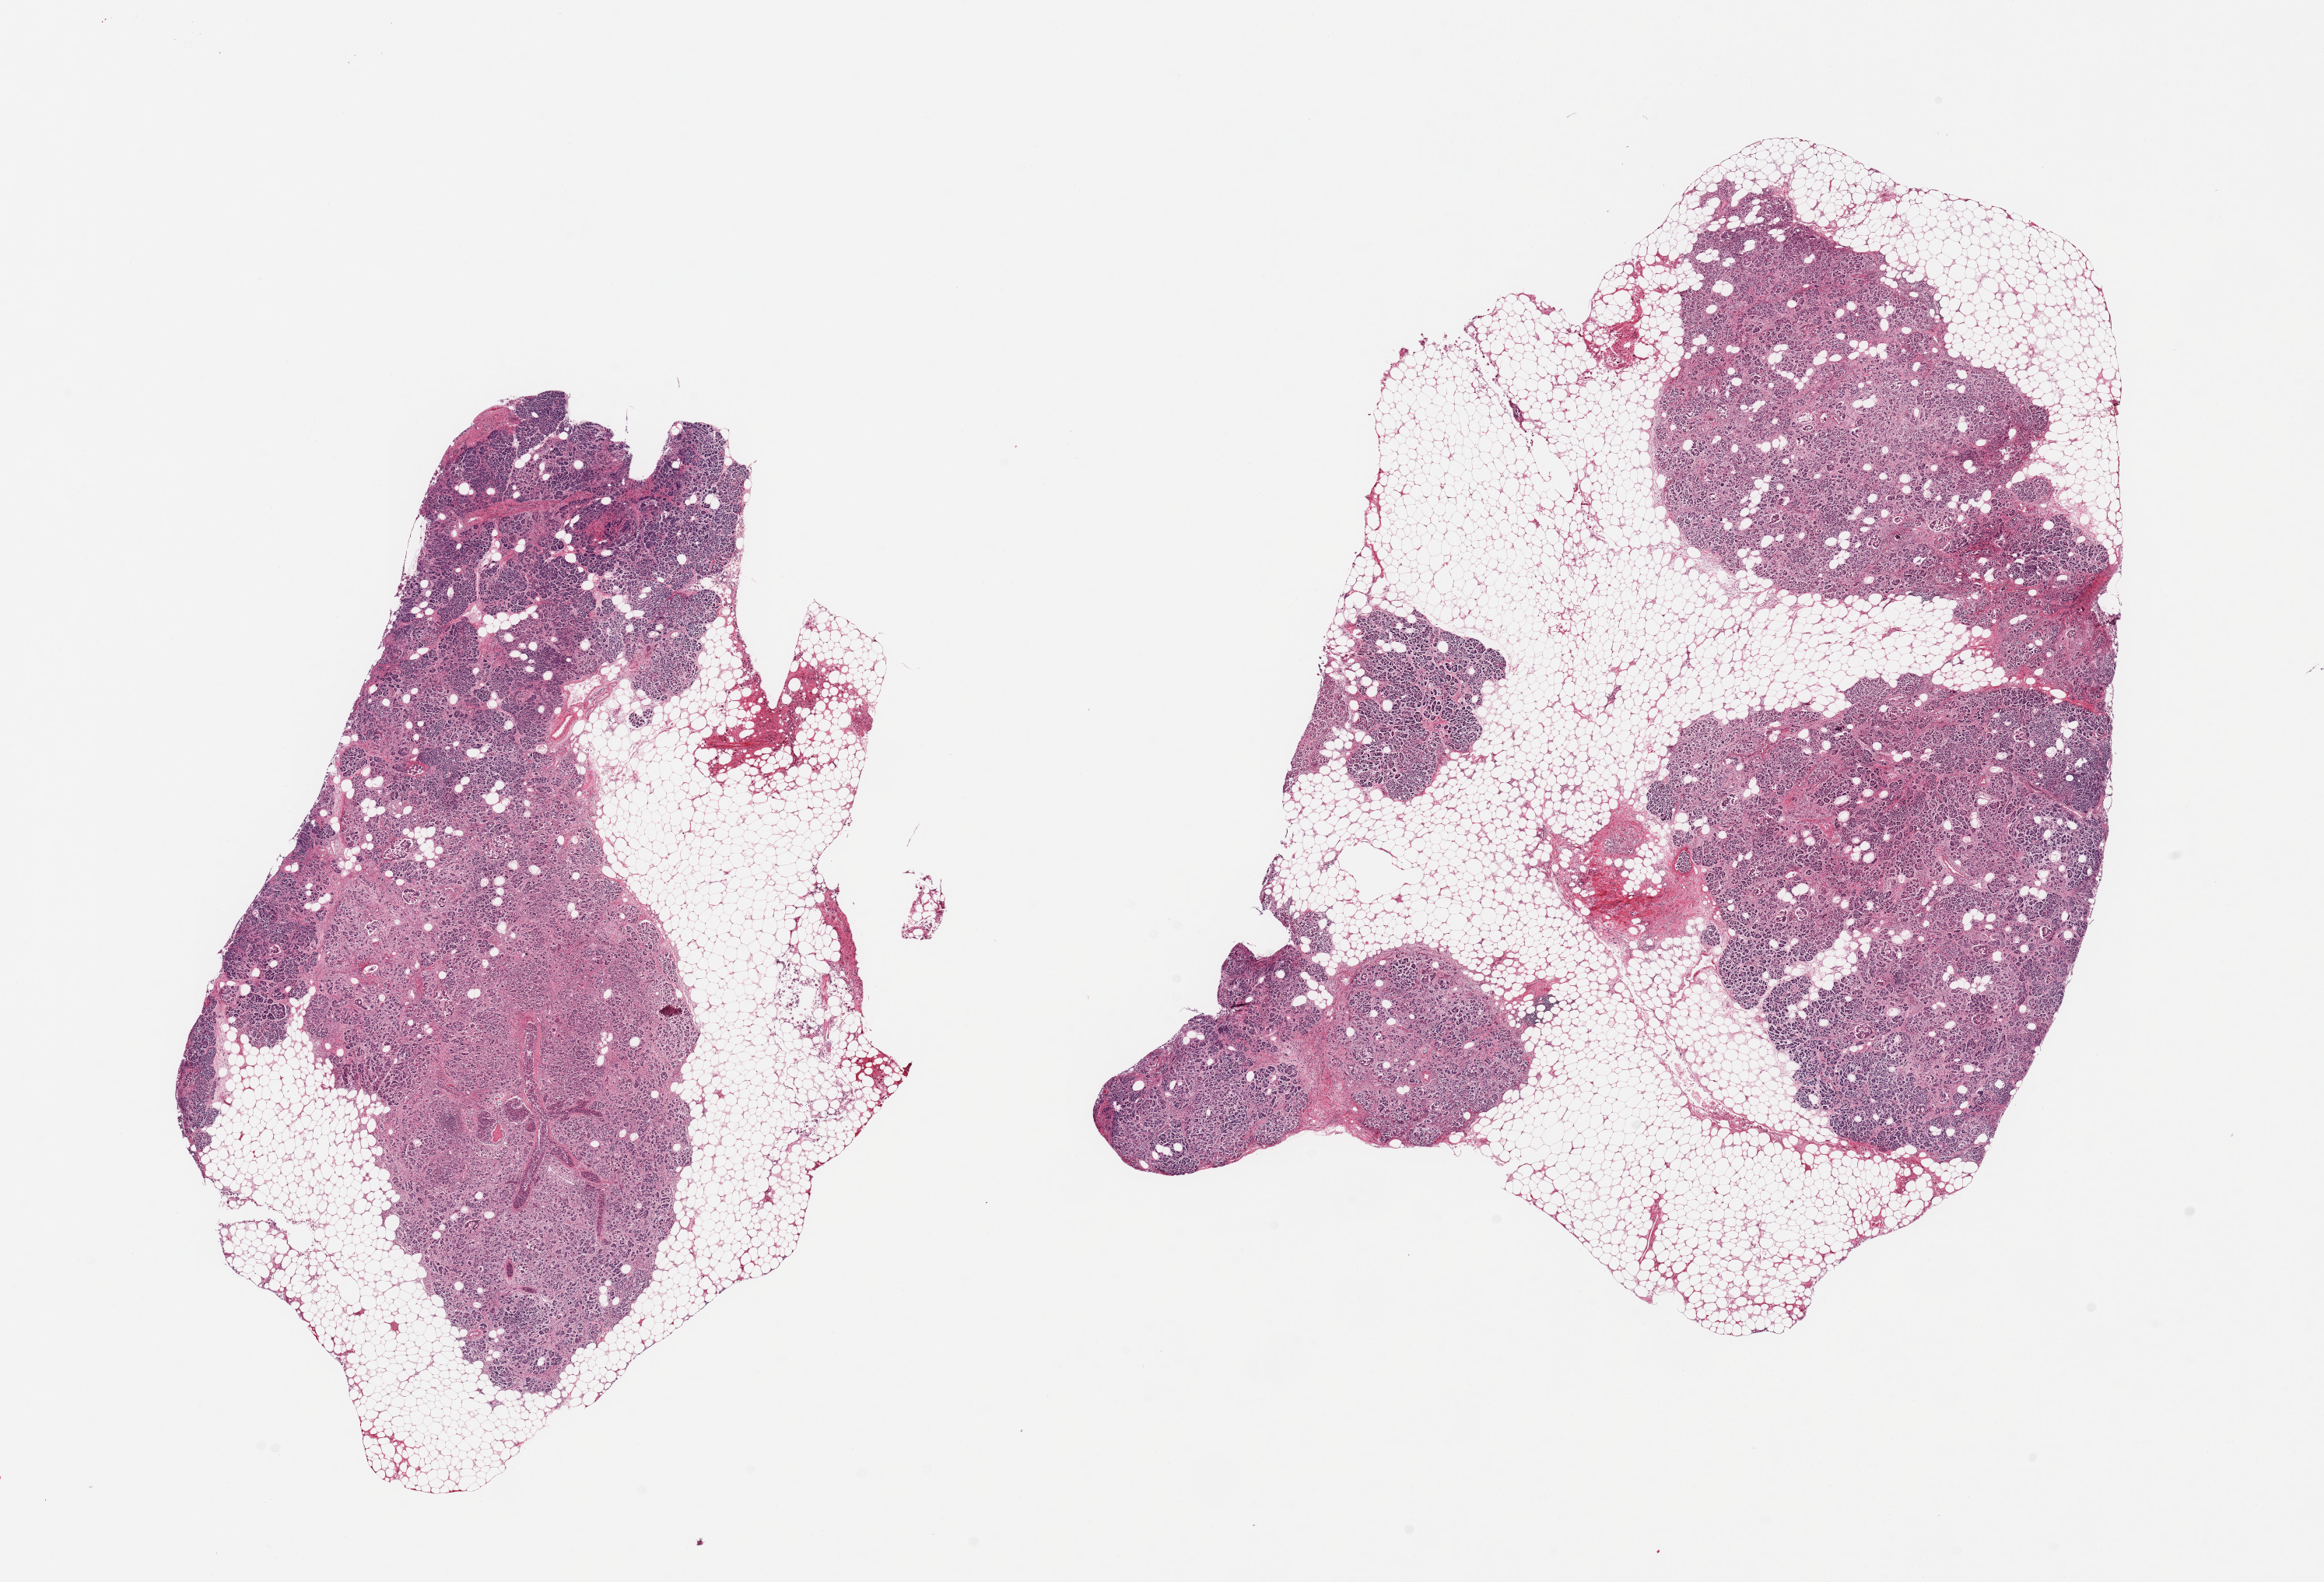
Haematoxylin and eosin whole-slide image — whole scanned area (about 23.6 x 16.1 mm) shown as a low-resolution overview. PAXgene-fixed, paraffin-embedded tissue. Section of pancreas (target tissue). Donor tissue sample. Male donor.
Pathologist's review note for this sample: 2 pieces, moderately advanced asponfication, Islets badly degraded, ~40% adherent/interstitial fat.